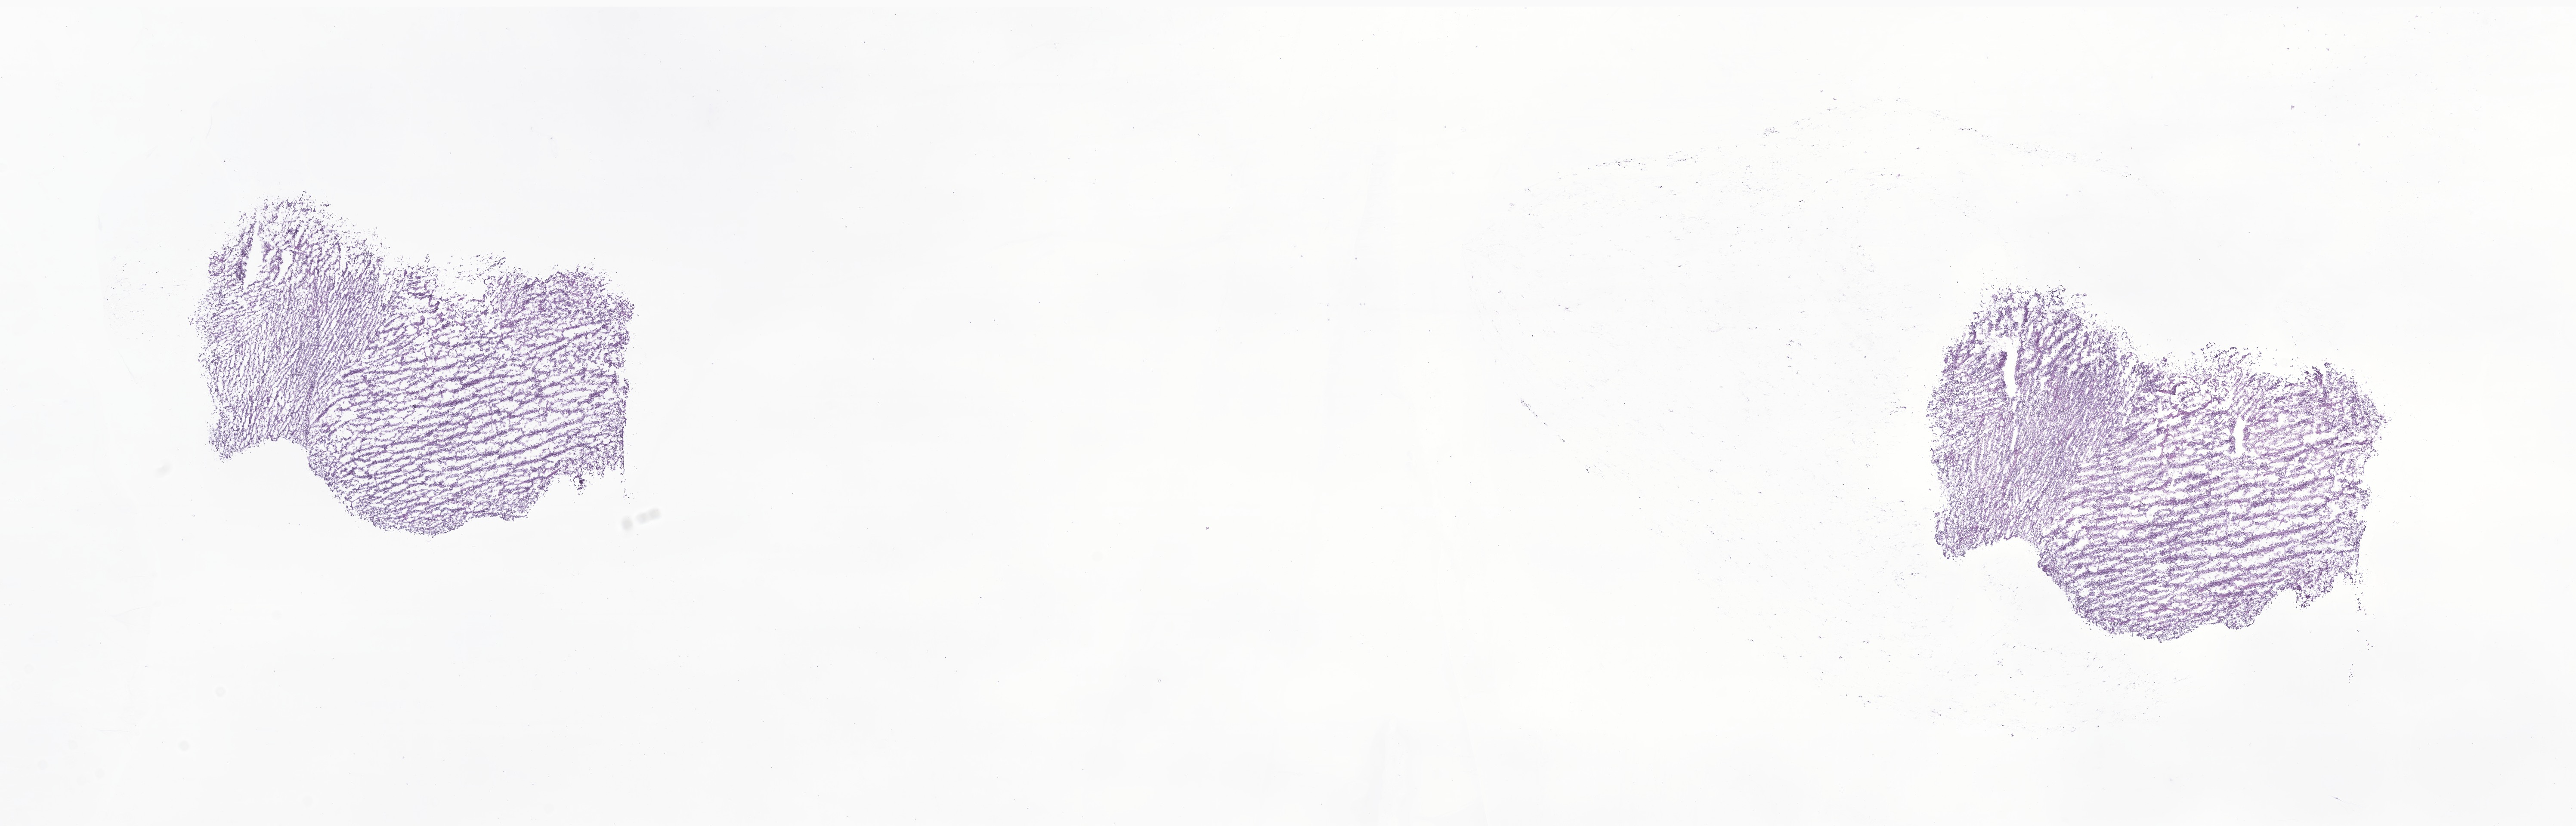
Digitized H&E-stained section of tumor tissue from the brain — shown as a low-resolution overview of the whole scanned area (about 25.2 x 8.1 mm). Frozen section. Male patient, age 678 days (about 1.9 years).
Recorded diagnosis: Medulloblastoma, NOS.